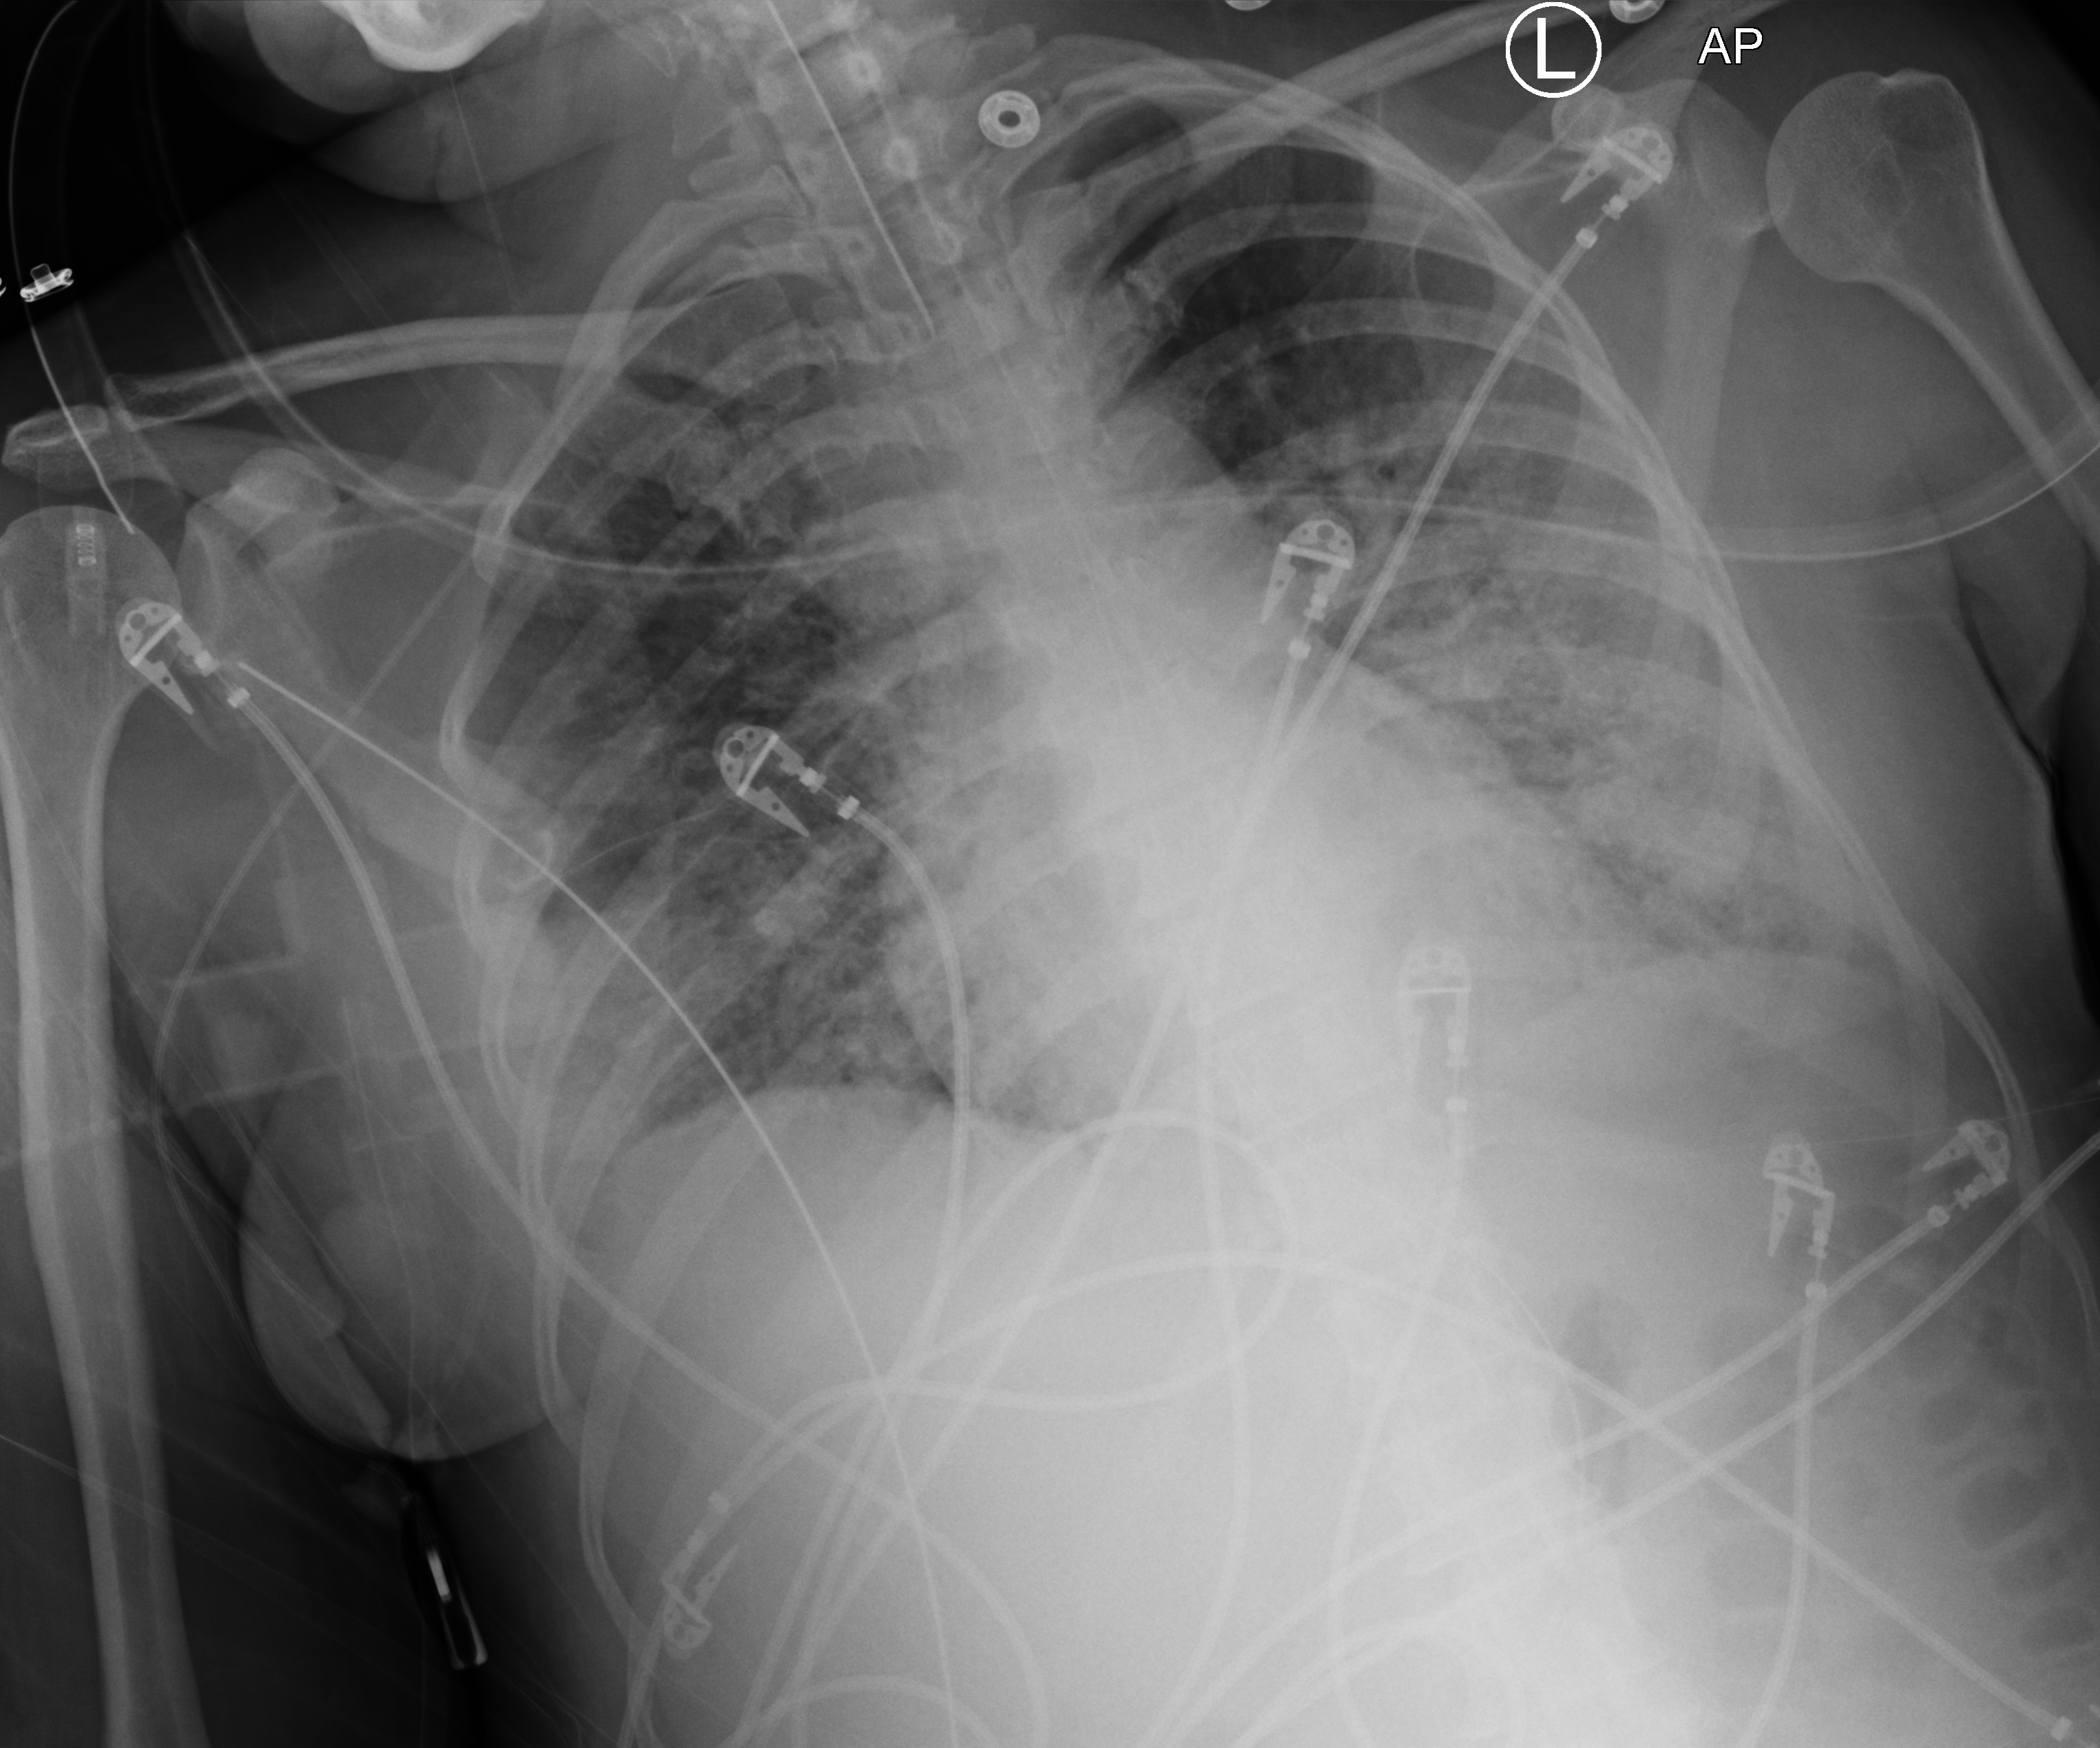
Bedside chest radiograph (computed radiography). Patient hospitalised with COVID-19; female, aged 18–59 years.
From the hospital-stay record, not from the radiograph (when in the stay this image was taken is not recorded):
- admitted to intensive care during this hospital stay: yes